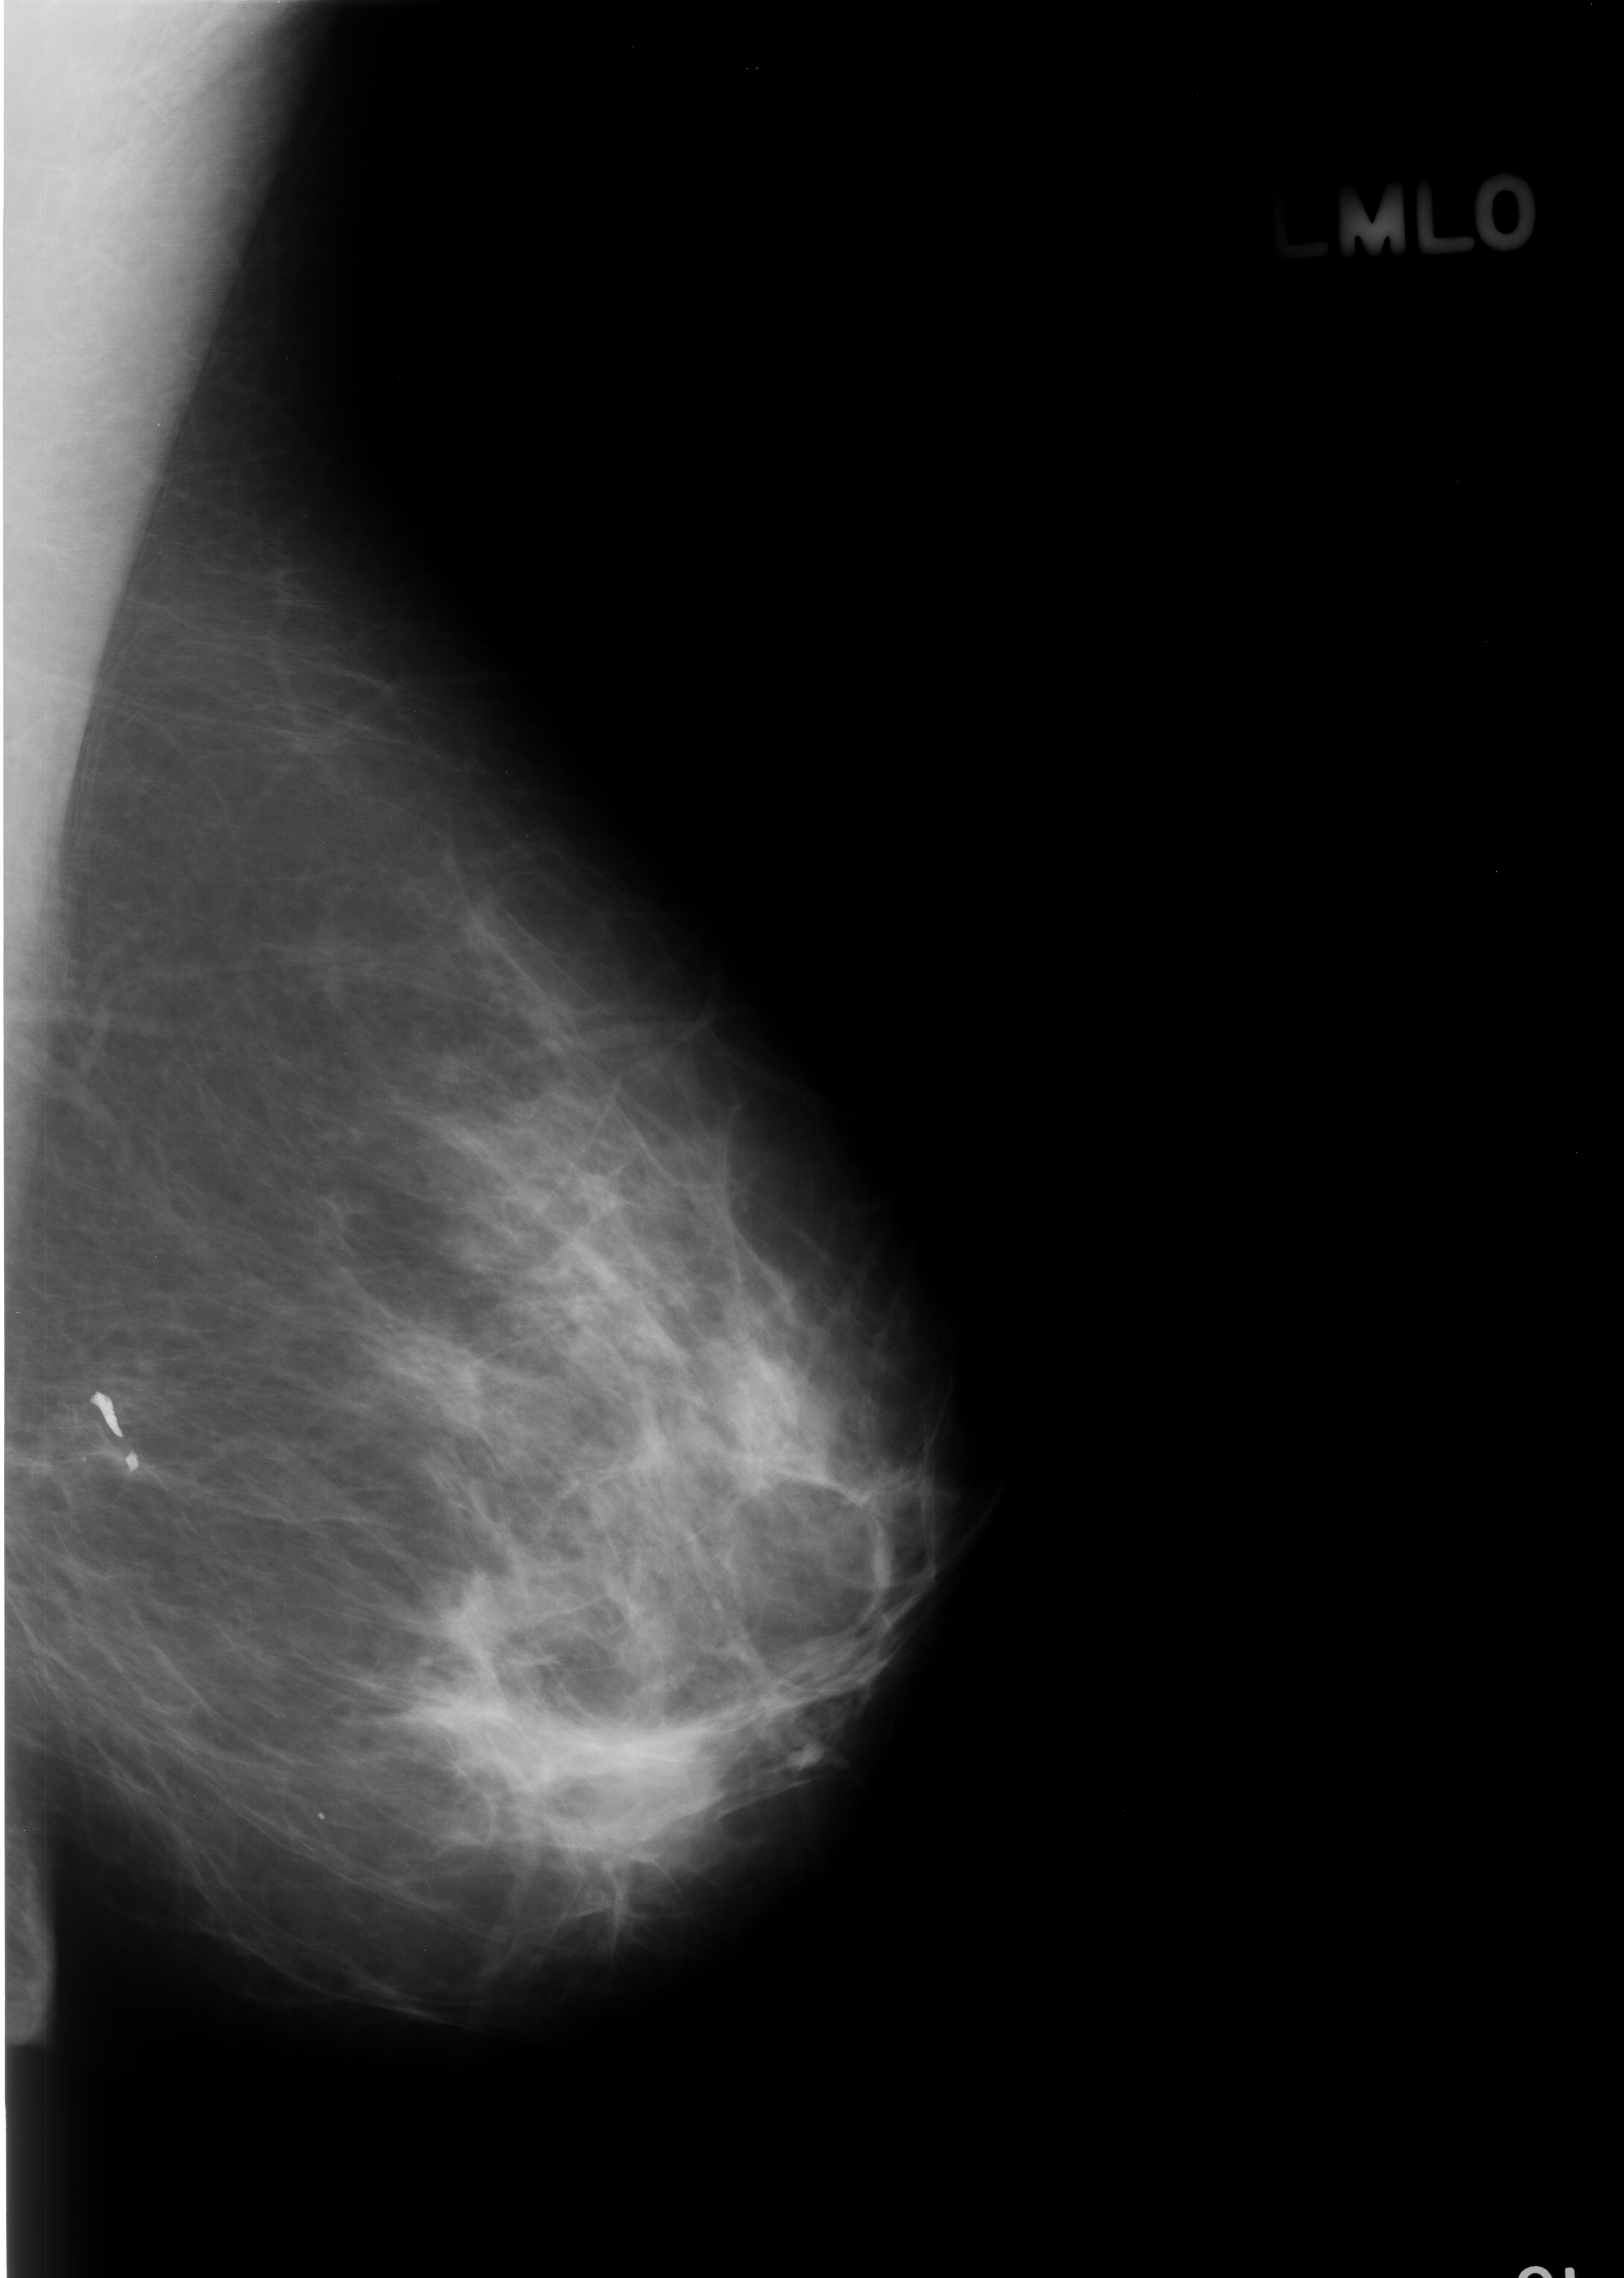
Scanned film-screen mammogram. Left breast. Mediolateral oblique (MLO) view. BI-RADS breast density category 2 (scale 1–4). 1624 × 2278 image matrix.
Marked abnormalities (boxes around the expert regions of interest):
- calcifications, distribution linear; BI-RADS assessment category 2; subtlety rating 5 on a 1 (subtle) to 5 (obvious) scale; pathology result (as recorded, not read from the image): benign: bounding box [x1, y1, x2, y2] px = [58, 1333, 184, 1511]